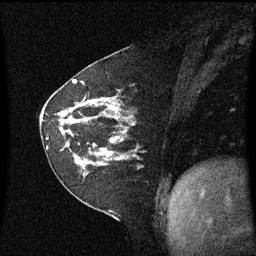
Breast MRI (dynamic contrast-enhanced), one sagittal slice. Slice 25 of 60 in the series (ordered by position). Dynamic contrast-enhanced series, image 2 of 3 at this slice position (ordered by acquisition). 1.5 T. TE 4.2 ms, TR 8.4 ms. 2 mm slice thickness. 256 × 256 image matrix, field of view 210 × 210 mm. Female patient, age 60 years. From the clinical record (not read from this slice): setting: breast cancer imaged before/during neoadjuvant chemotherapy; receptor status: triple-negative.
Outlined on this slice (semi-automatically segmented with operator editing):
- analysis volume of interest (the breast-tissue region the enhancement analysis was run in; not a lesion): bounding box (x1, y1, x2, y2) in pixels: (45, 99, 138, 182)
- tumour enhancement mask (voxels above the 70 % enhancement threshold inside the analysis volume of interest): (62, 101, 118, 157)